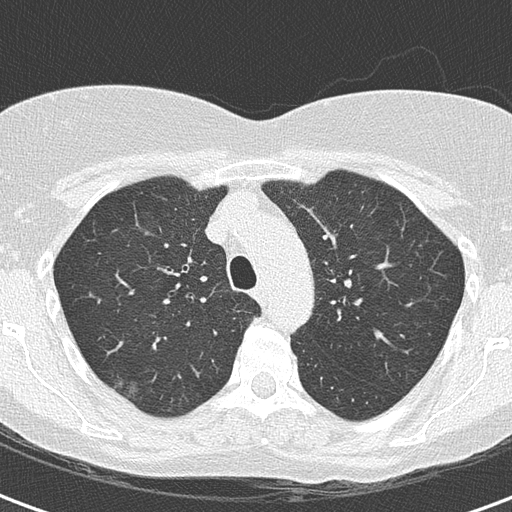
Chest CT (low-dose screening protocol), one axial image. Second screening round (one year after baseline). Lung window (W 1500 / L -600 HU). Slice 43 of 172 in the series. 512 × 512 image matrix, field of view 283 × 283 mm. Female, age 56 years at enrolment. Current smoker at enrolment.
Expert reader's lesion annotation, box from (x=95, y=363) to (x=152, y=413) px. Screening reader's record for this exam (one nodule recorded; not confirmed to be the boxed lesion): non-calcified nodule or mass ≥4 mm, right upper lobe, 18 × 18 mm, mixed attenuation, pre-existing on the prior screen: yes. Later outcome: lung cancer diagnosed 93 days after this screen — bronchiolo-alveolar adenocarcinoma, NOS, right upper lobe, well differentiated (G1), stage IA (AJCC 6th edition), 15 mm at pathology.